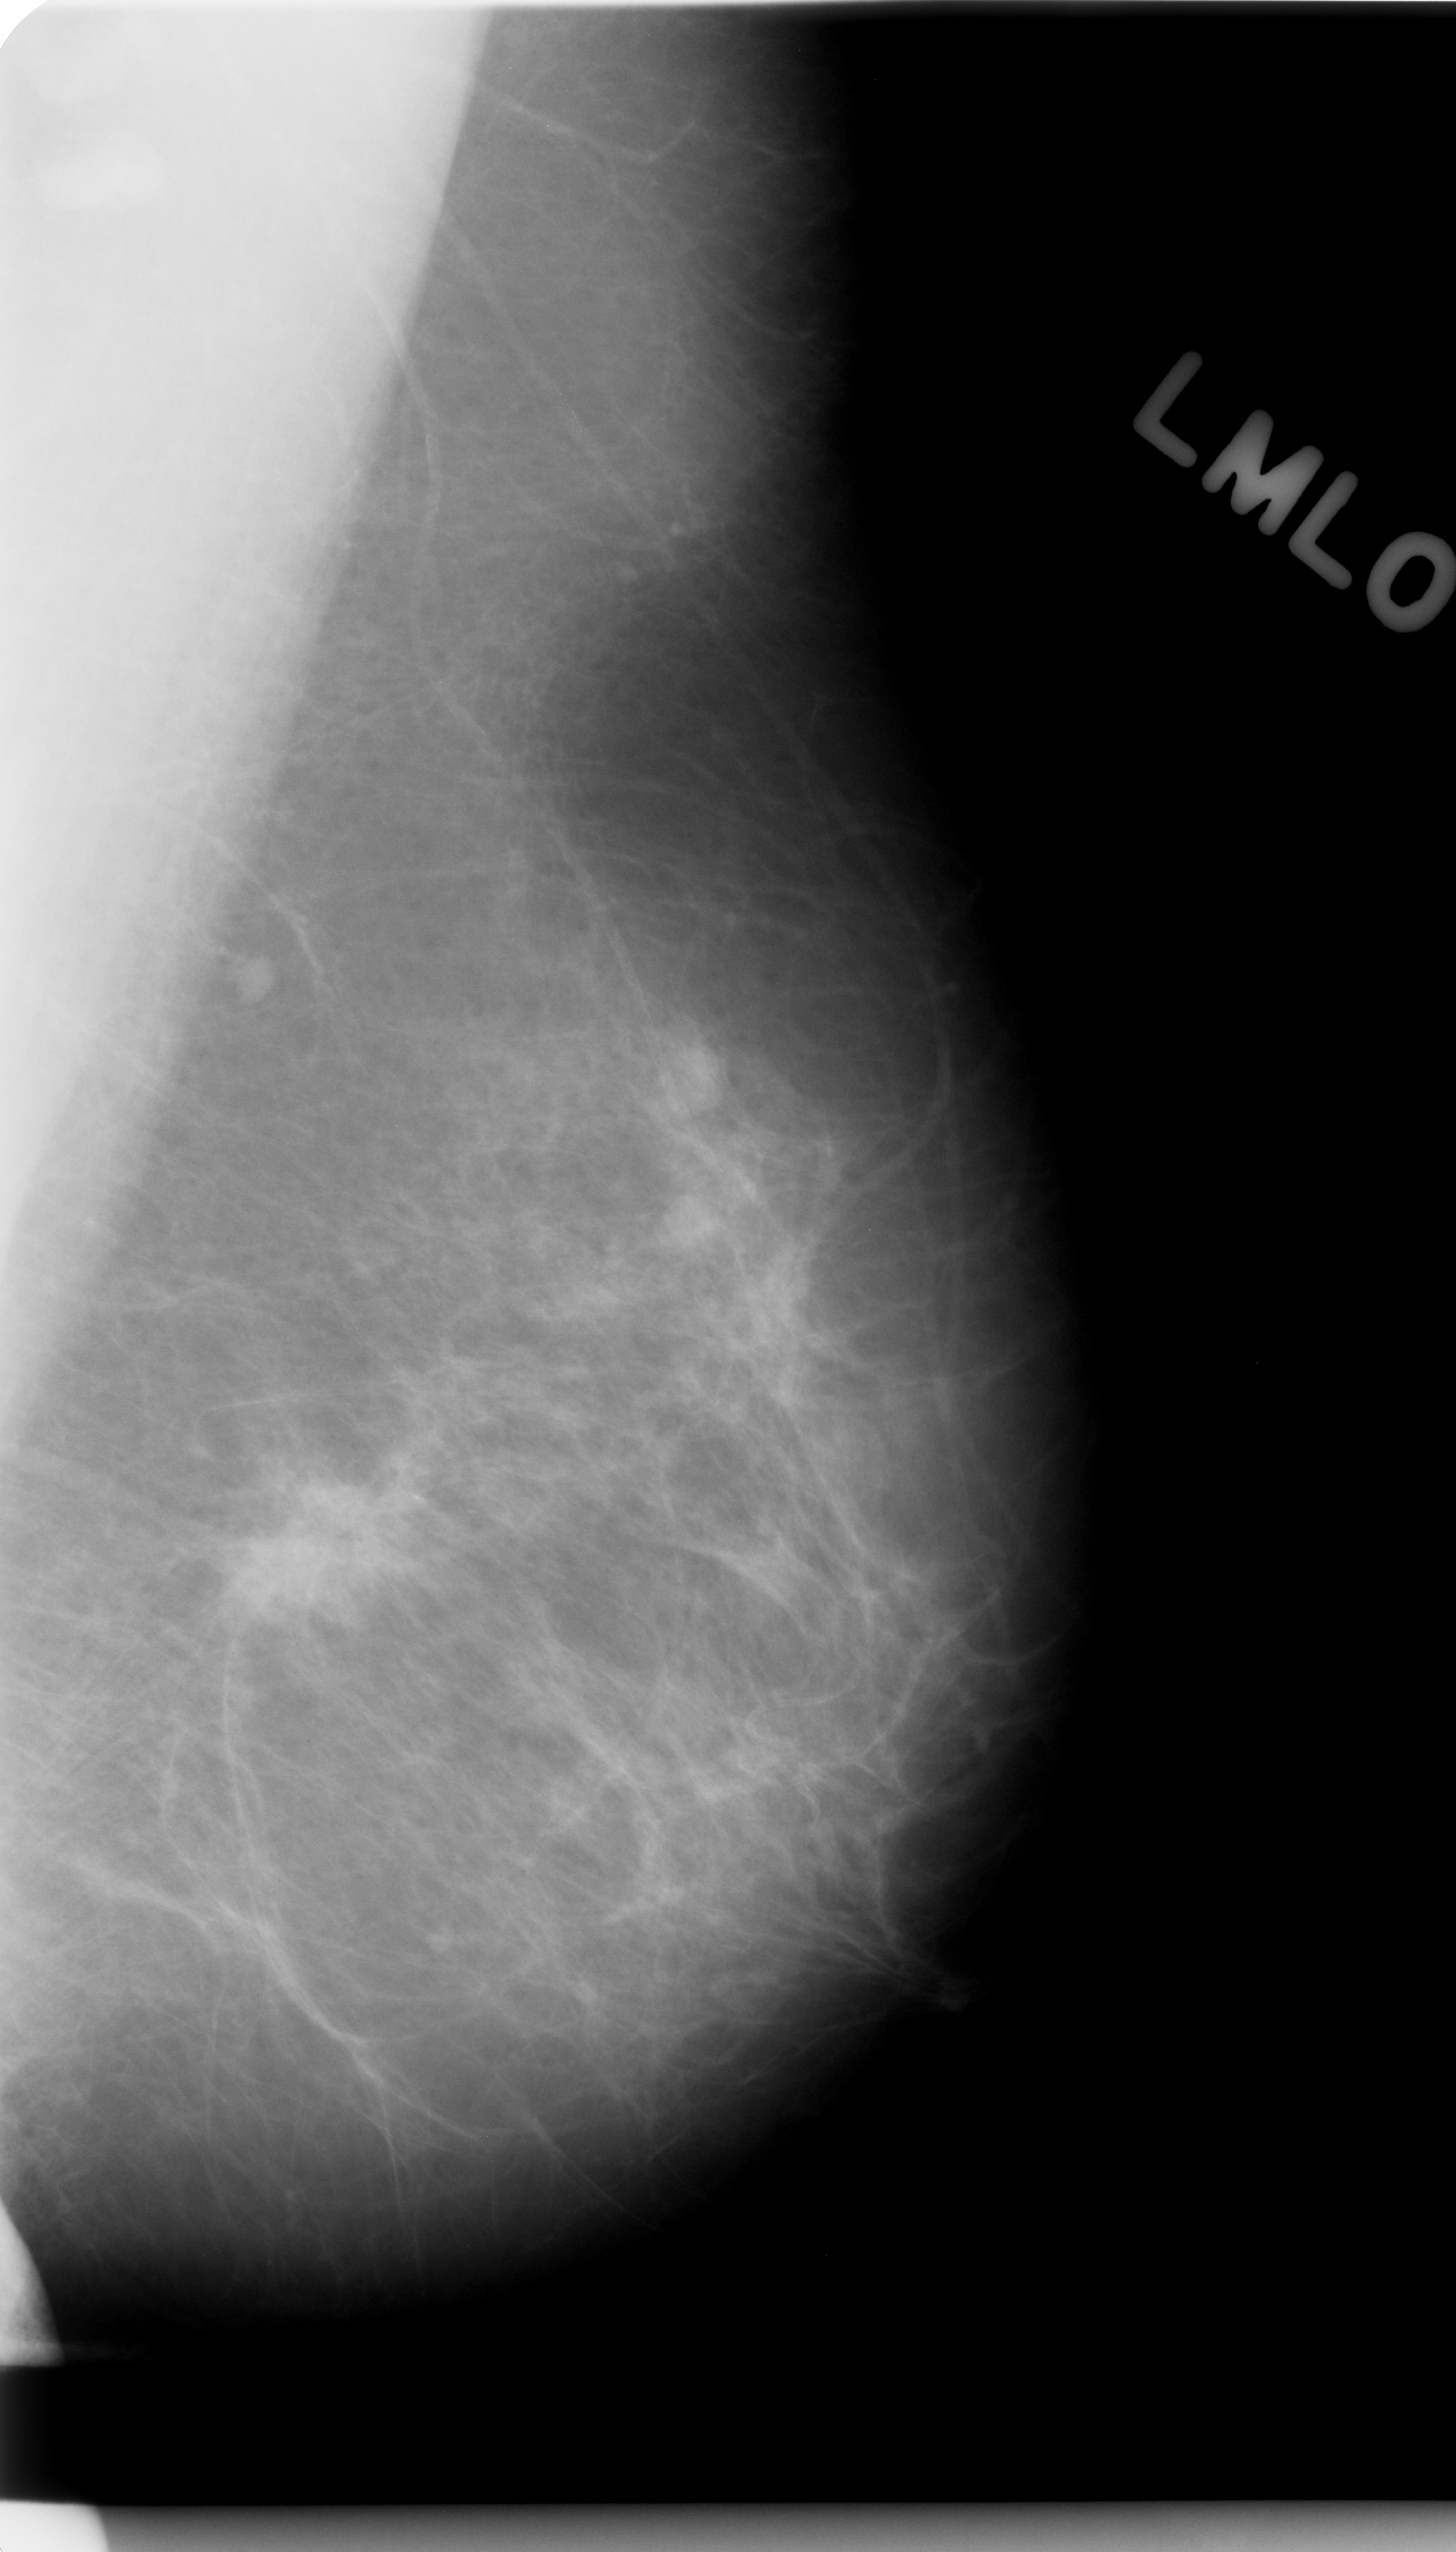
Scanned film-screen mammogram; left breast; MLO view.
Marked abnormality: mass, shape irregular, margins spiculated; BI-RADS assessment category 5; pathology (as recorded): malignant.